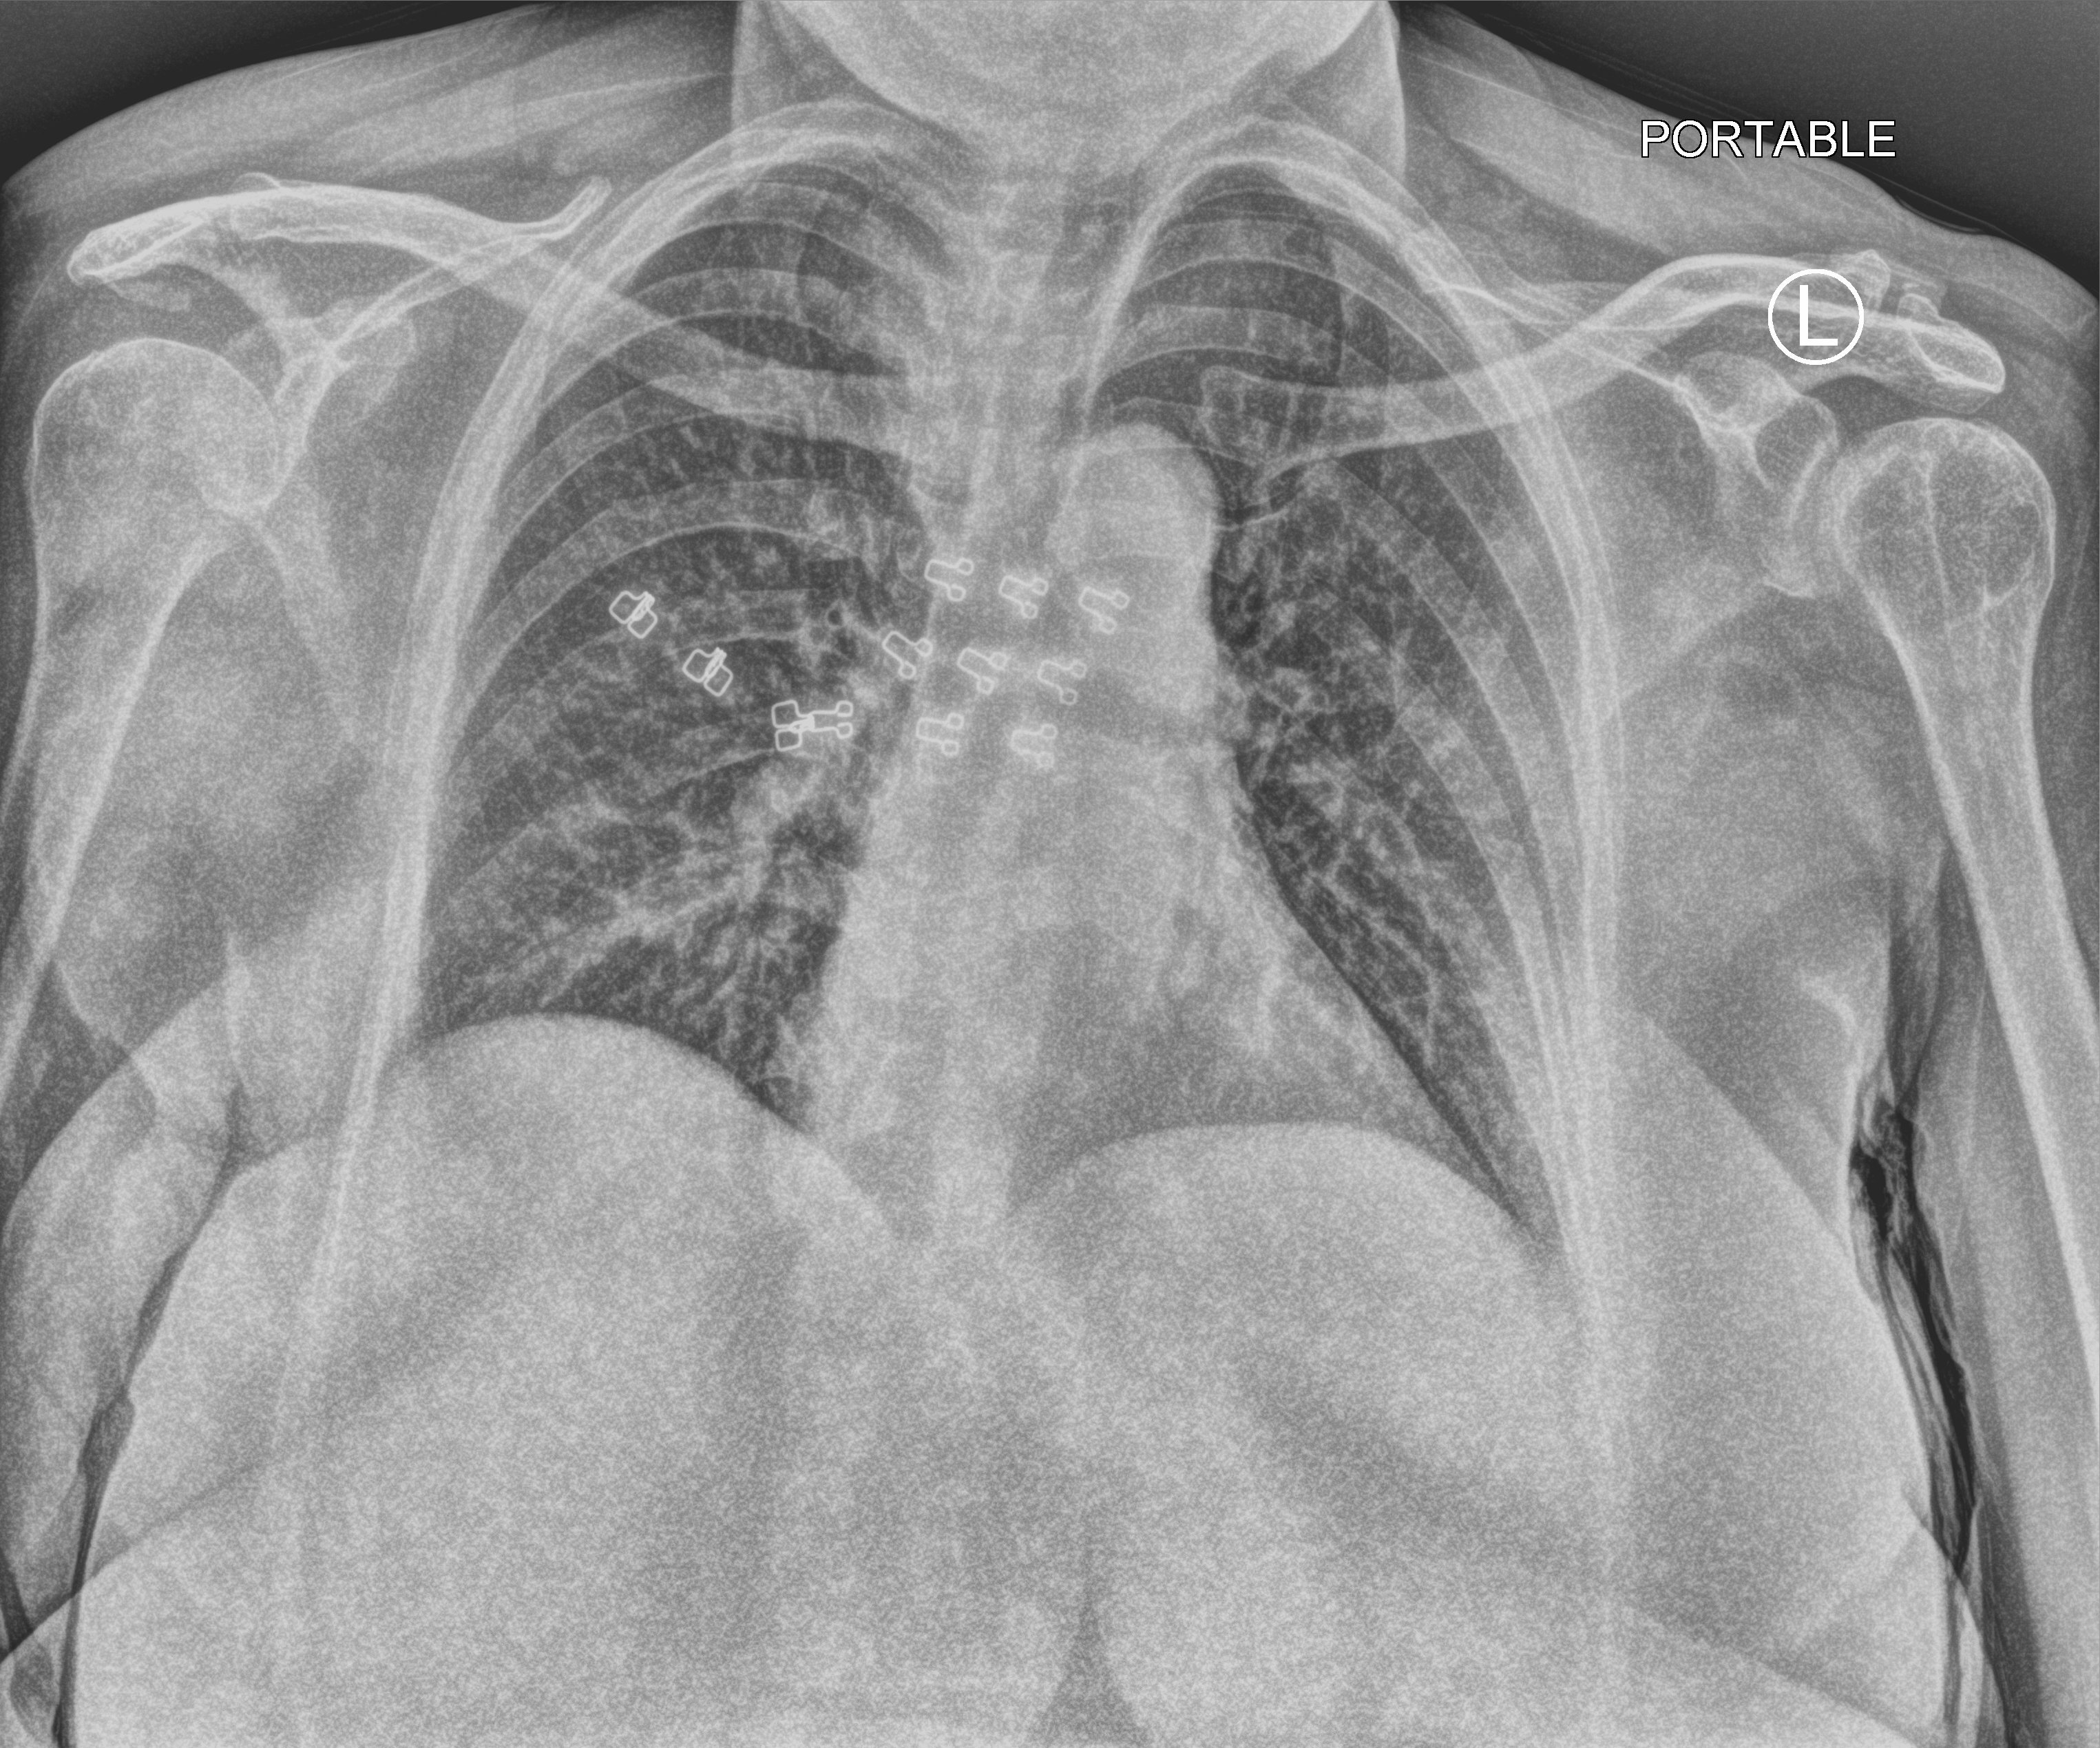
Chest X-ray (portable), anteroposterior (AP) projection. Female patient hospitalised with COVID-19, age 60–74 years.
Hospital-stay facts (about this admission, not read from this image; timing relative to this image not recorded):
- admitted to intensive care during this hospital stay: no
- chronic kidney disease (admission record): no
- length of hospital stay: 3 days